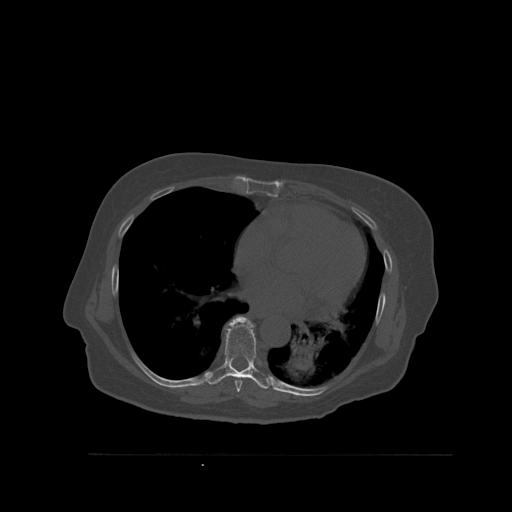
CT including the spine, one axial slice. Position 353 of 527 along the scan axis. Bone window (W 1800 / L 400 HU). 1.5 mm slice thickness. 512 × 512 image matrix, field of view 470 × 470 mm. Patient: female, 73 years. From the clinical record (not read from this slice): primary cancer: breast.
Outlined on this slice (semi-automatic segmentation, software-assisted and operator-edited):
- T7 vertebra: bounding box [x1, y1, x2, y2] px = [235, 378, 253, 393]
- T8 vertebra: [207, 316, 269, 389]